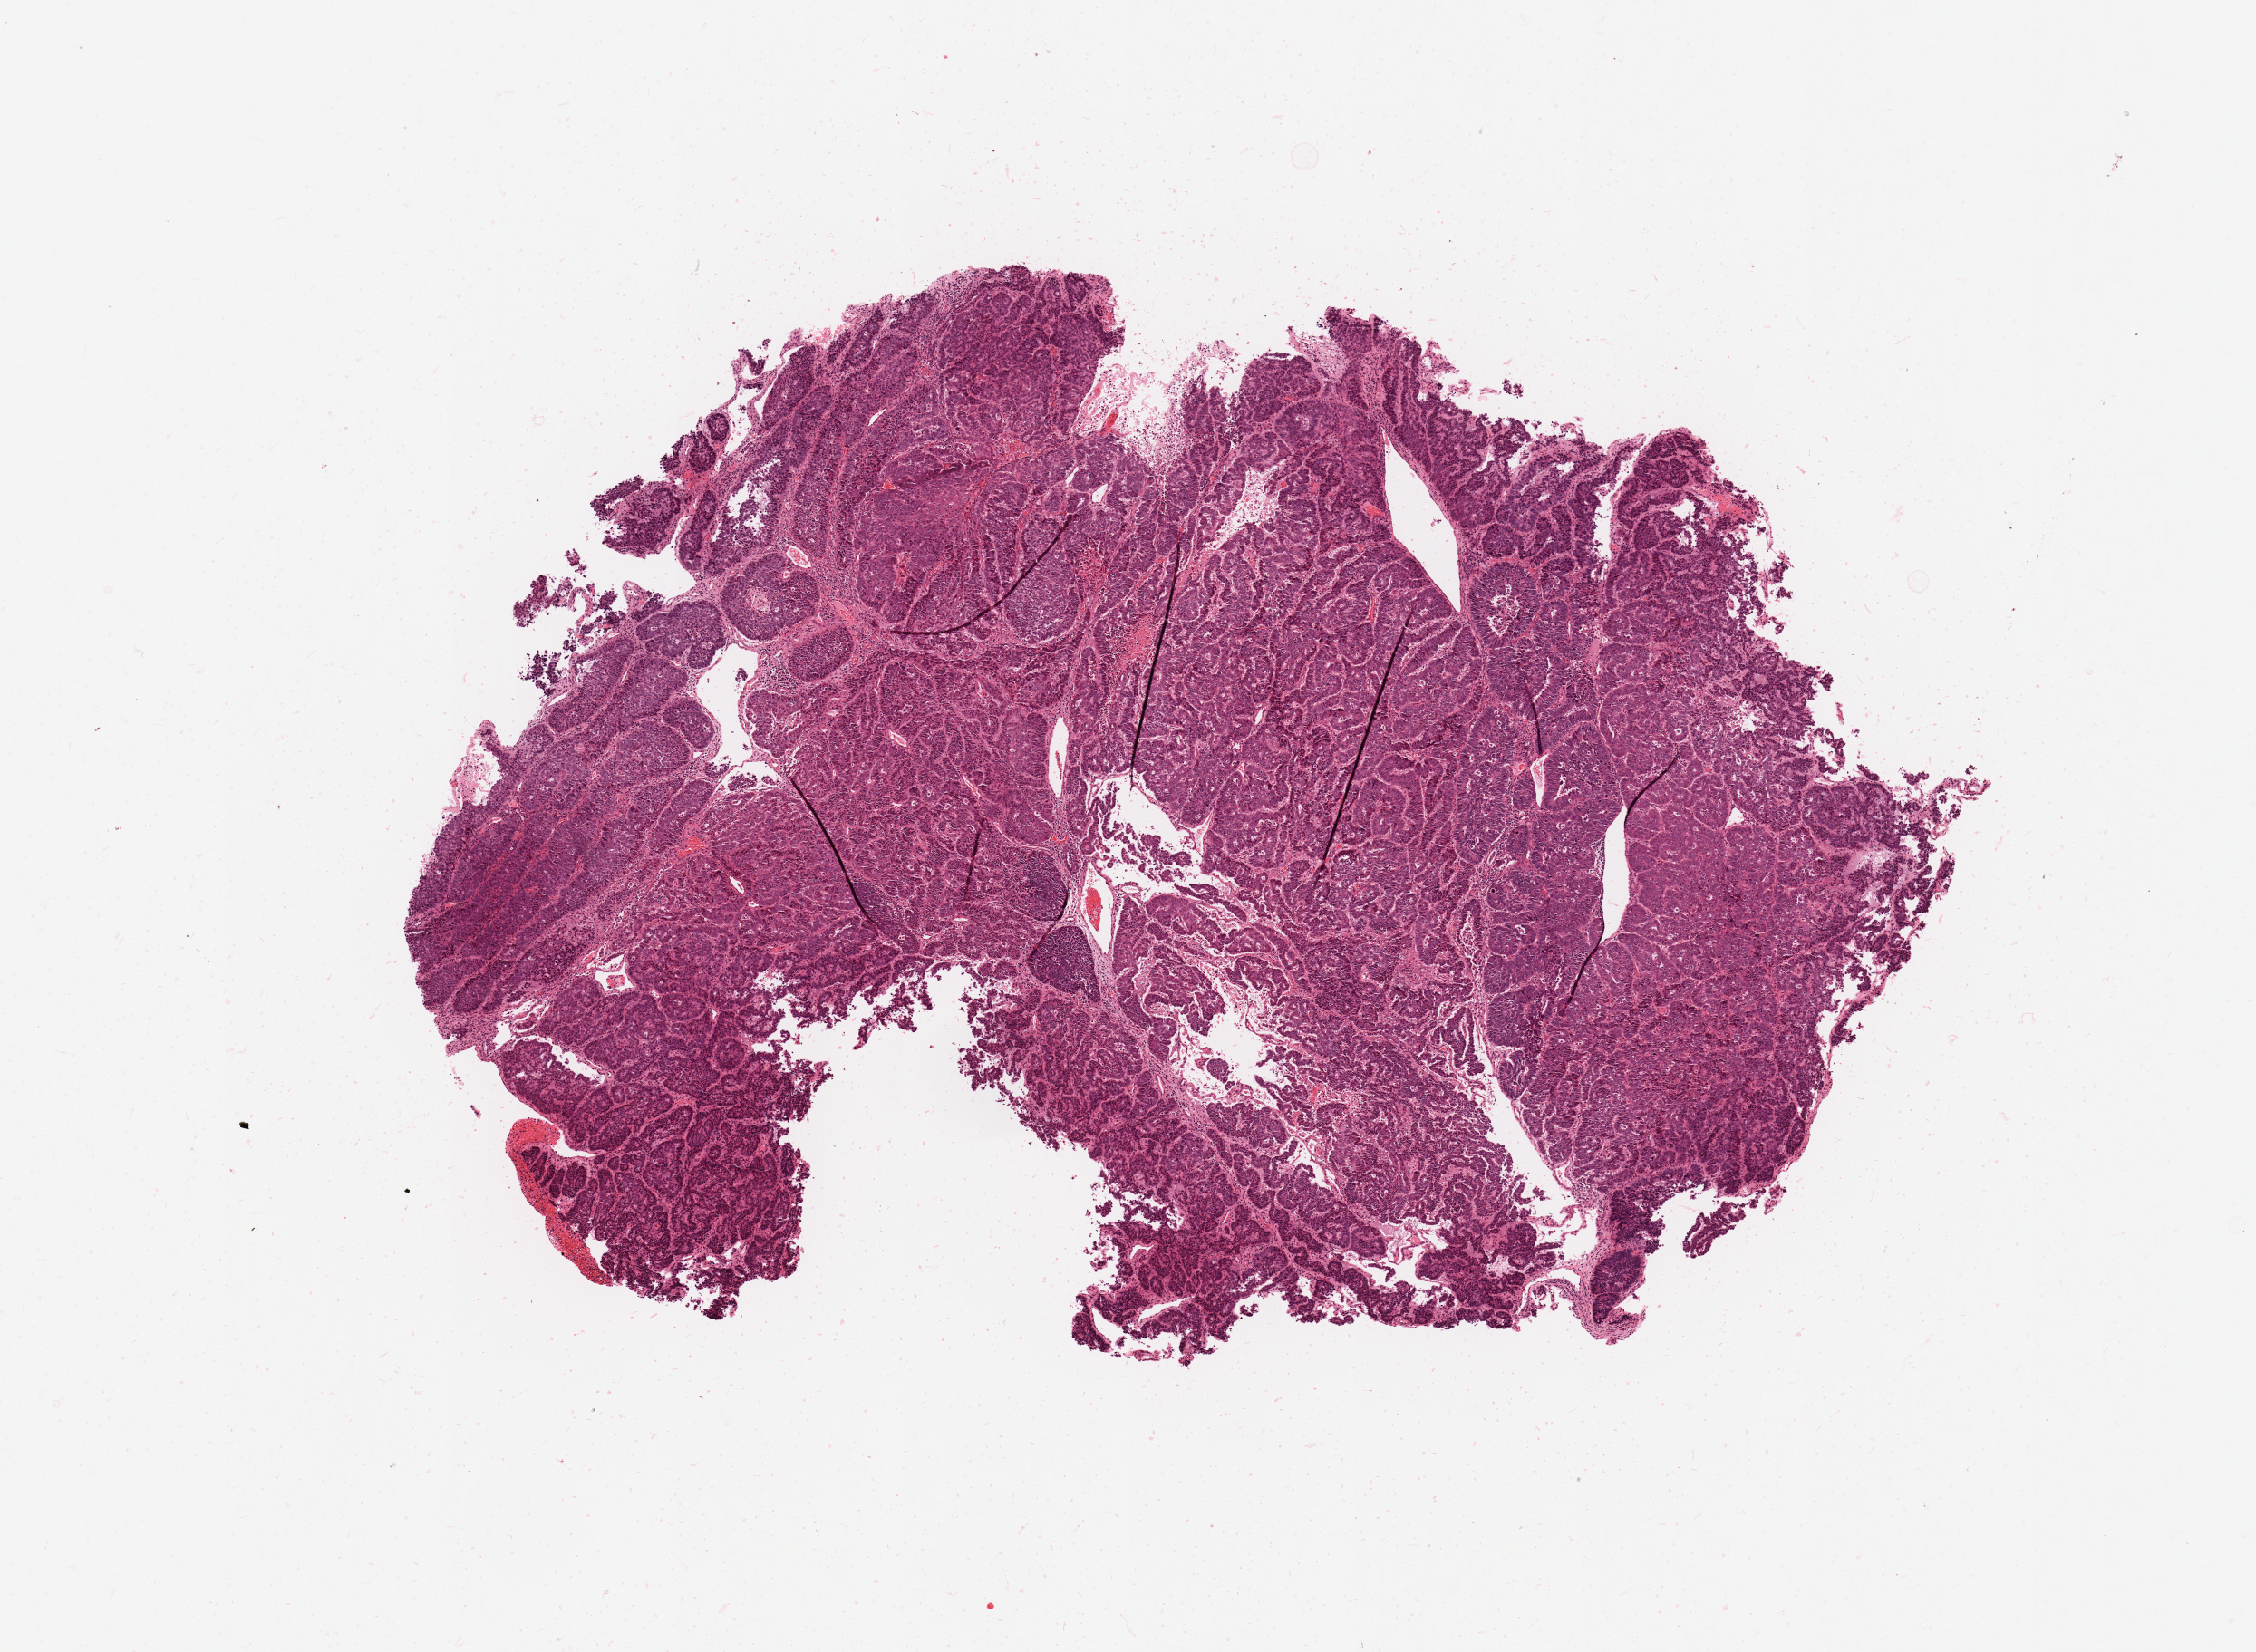
H&E whole-slide image, shown as a low-resolution overview of the whole scanned area (about 9.8 x 7.2 mm, acquisition: 20x scan); uterus, tumour tissue. 73-year-old female patient.
Histologic diagnosis: Endometrioid adenocarcinoma, NOS.